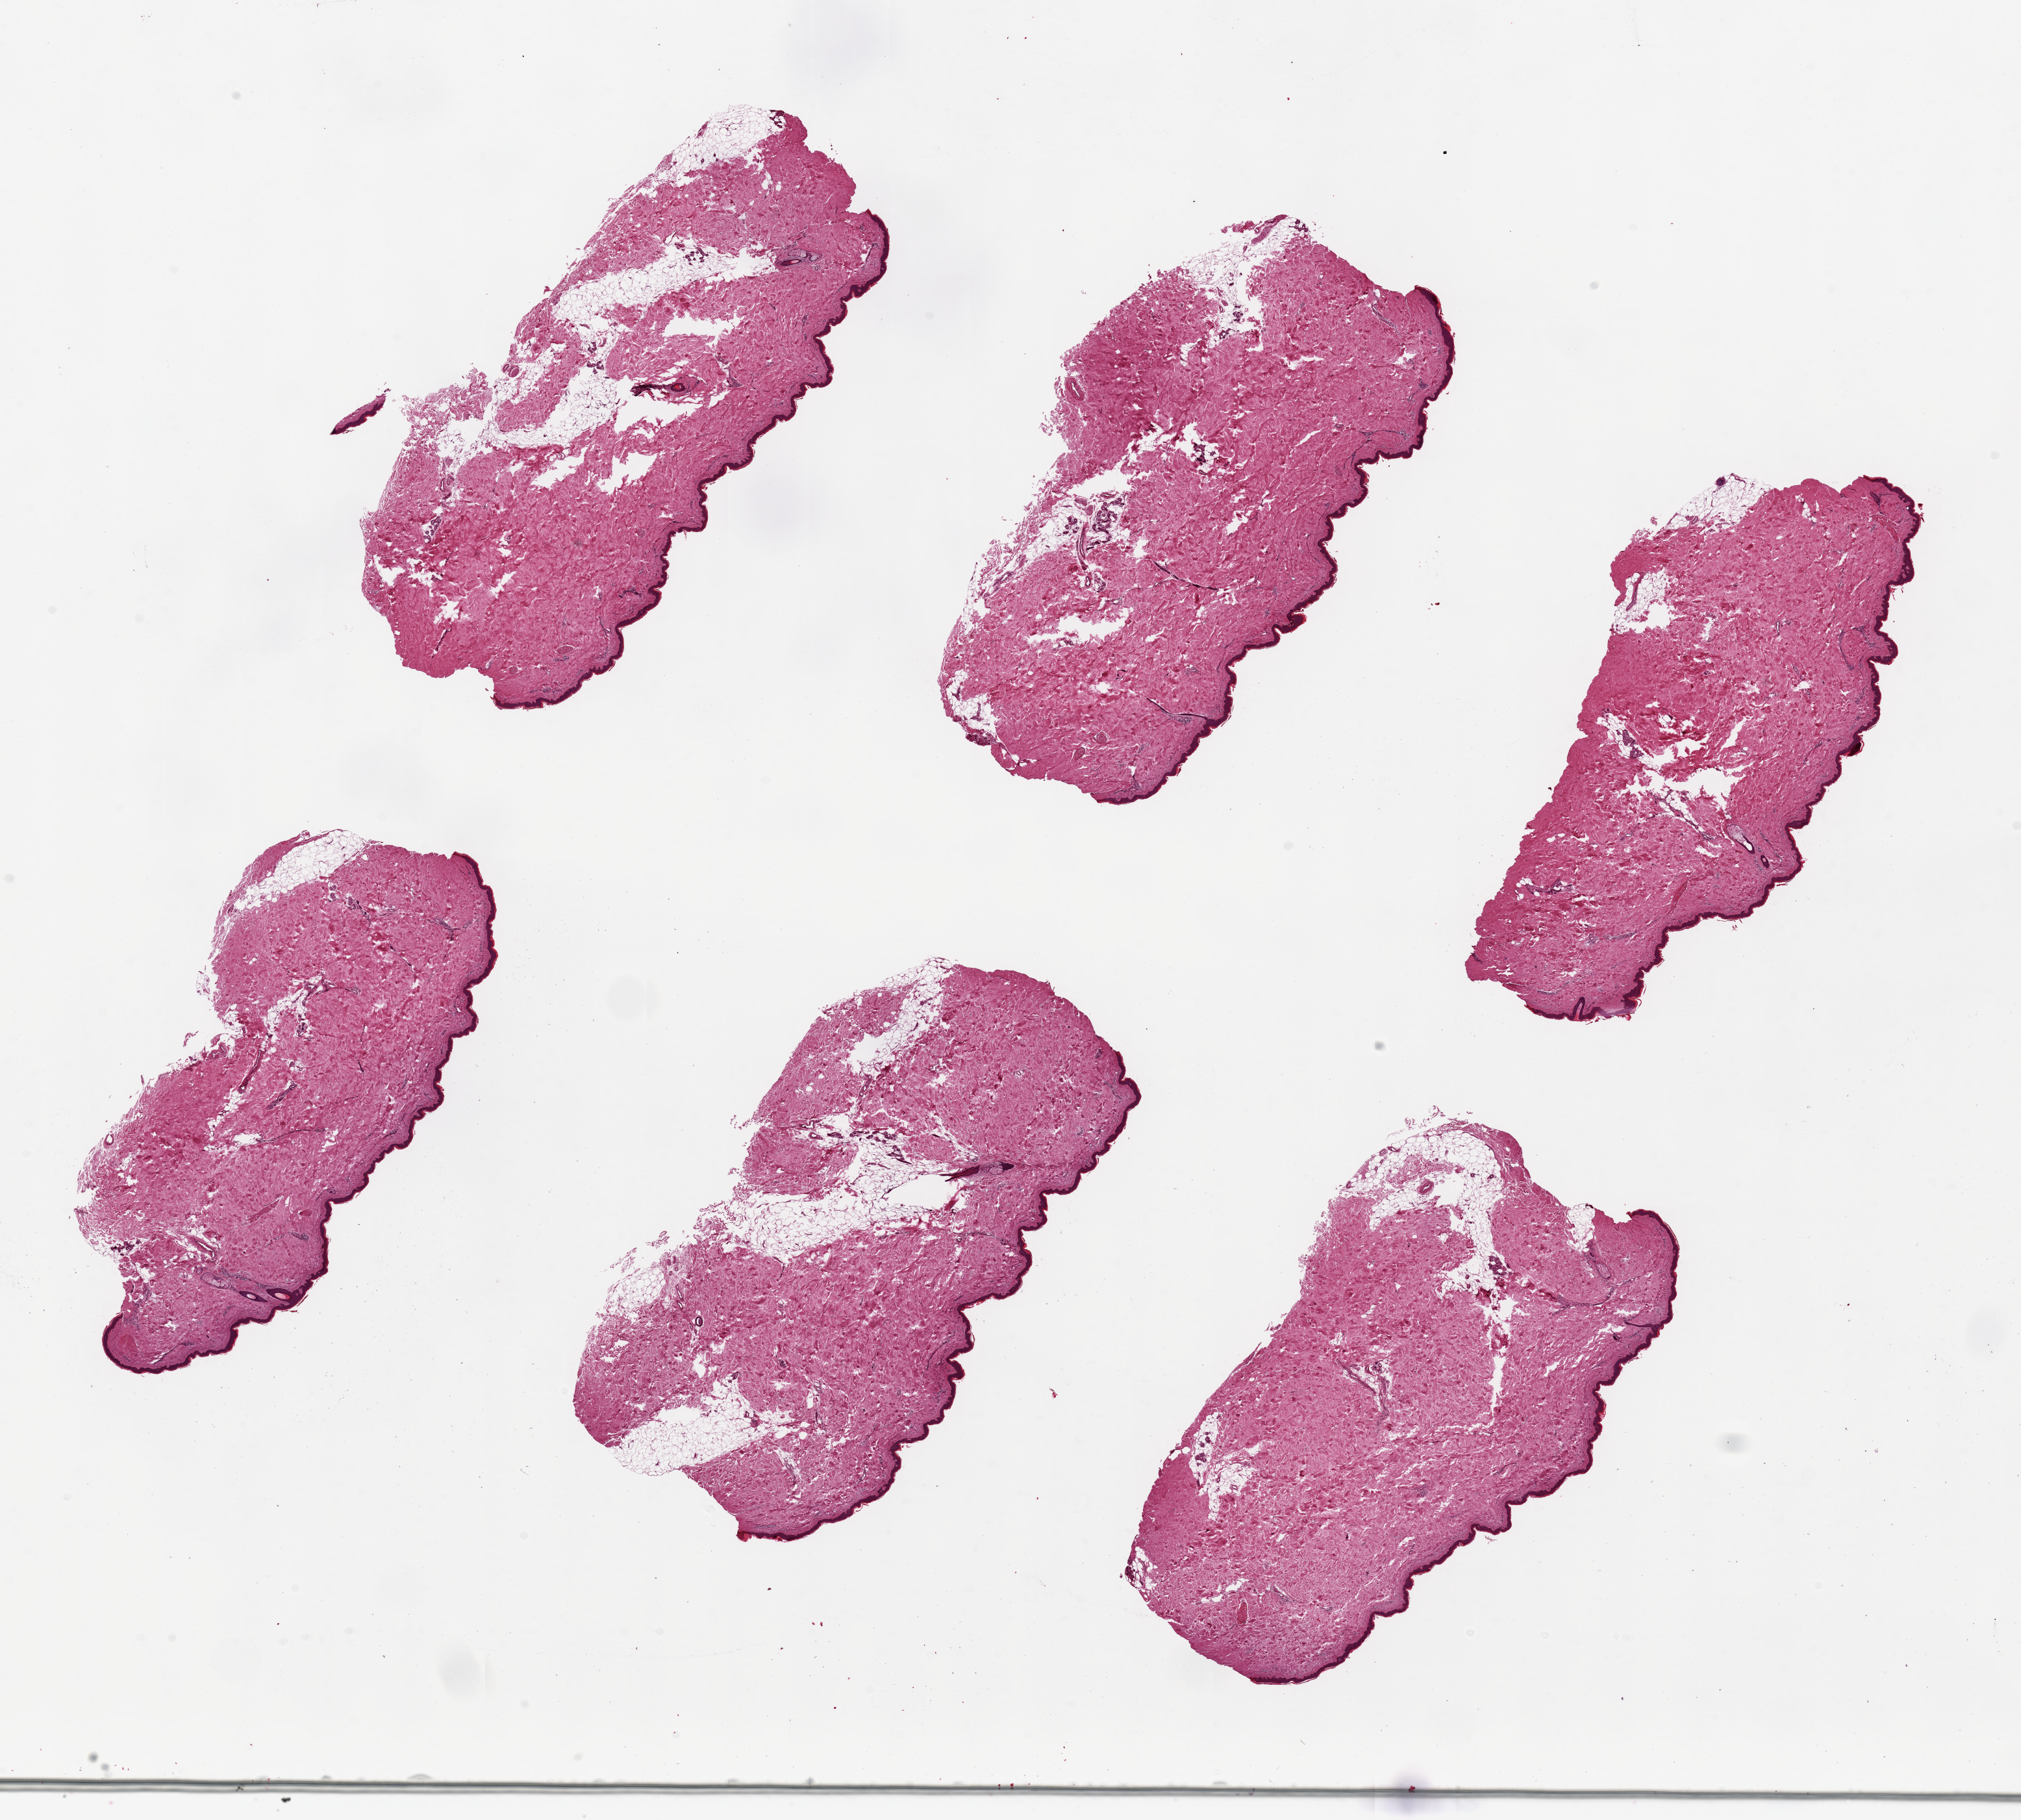
Hematoxylin and eosin (H&E) whole-slide image — whole scanned area (about 24.6 x 22.2 mm, from a 20x scan) shown as a low-resolution overview. PAXgene-fixed, paraffin-embedded tissue. Sampled site (target tissue): skin of lower leg. Tissue donor sample. Donor sex: female.
Reviewer comment on this tissue sample: 6 pieces, ~ 7.5x3mm, squamous epithelium is ~2-3% of thickness.